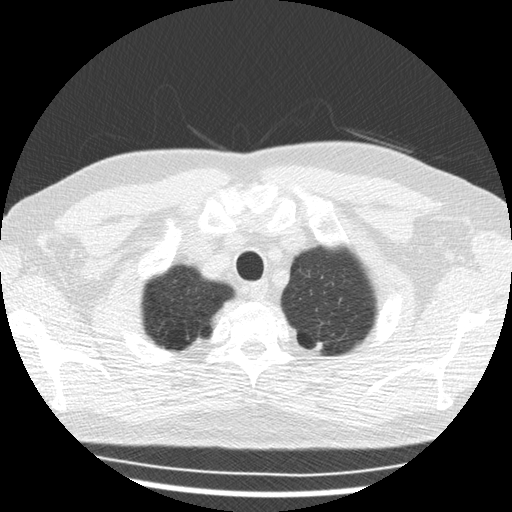
Chest CT (low-dose screening protocol), one axial image; baseline screening round; lung window (W 1500 / L -600 HU); standard (soft-tissue) reconstruction kernel (STANDARD); slice 30 of 168 in the series; 512 × 512 image matrix. Male participant, aged 57 years at enrolment. Former smoker at enrolment.
Expert-annotated lung lesion, box from (x=306, y=334) to (x=333, y=357) px. Screening reader's record for this exam (one nodule recorded; not confirmed to be the boxed lesion): non-calcified nodule or mass ≥4 mm, right upper lobe, 7 × 6 mm, smooth margins, soft tissue attenuation. Note: the box lies in the patient's left hemithorax on this image, whereas the reader's record names the right lung; they may be different findings.